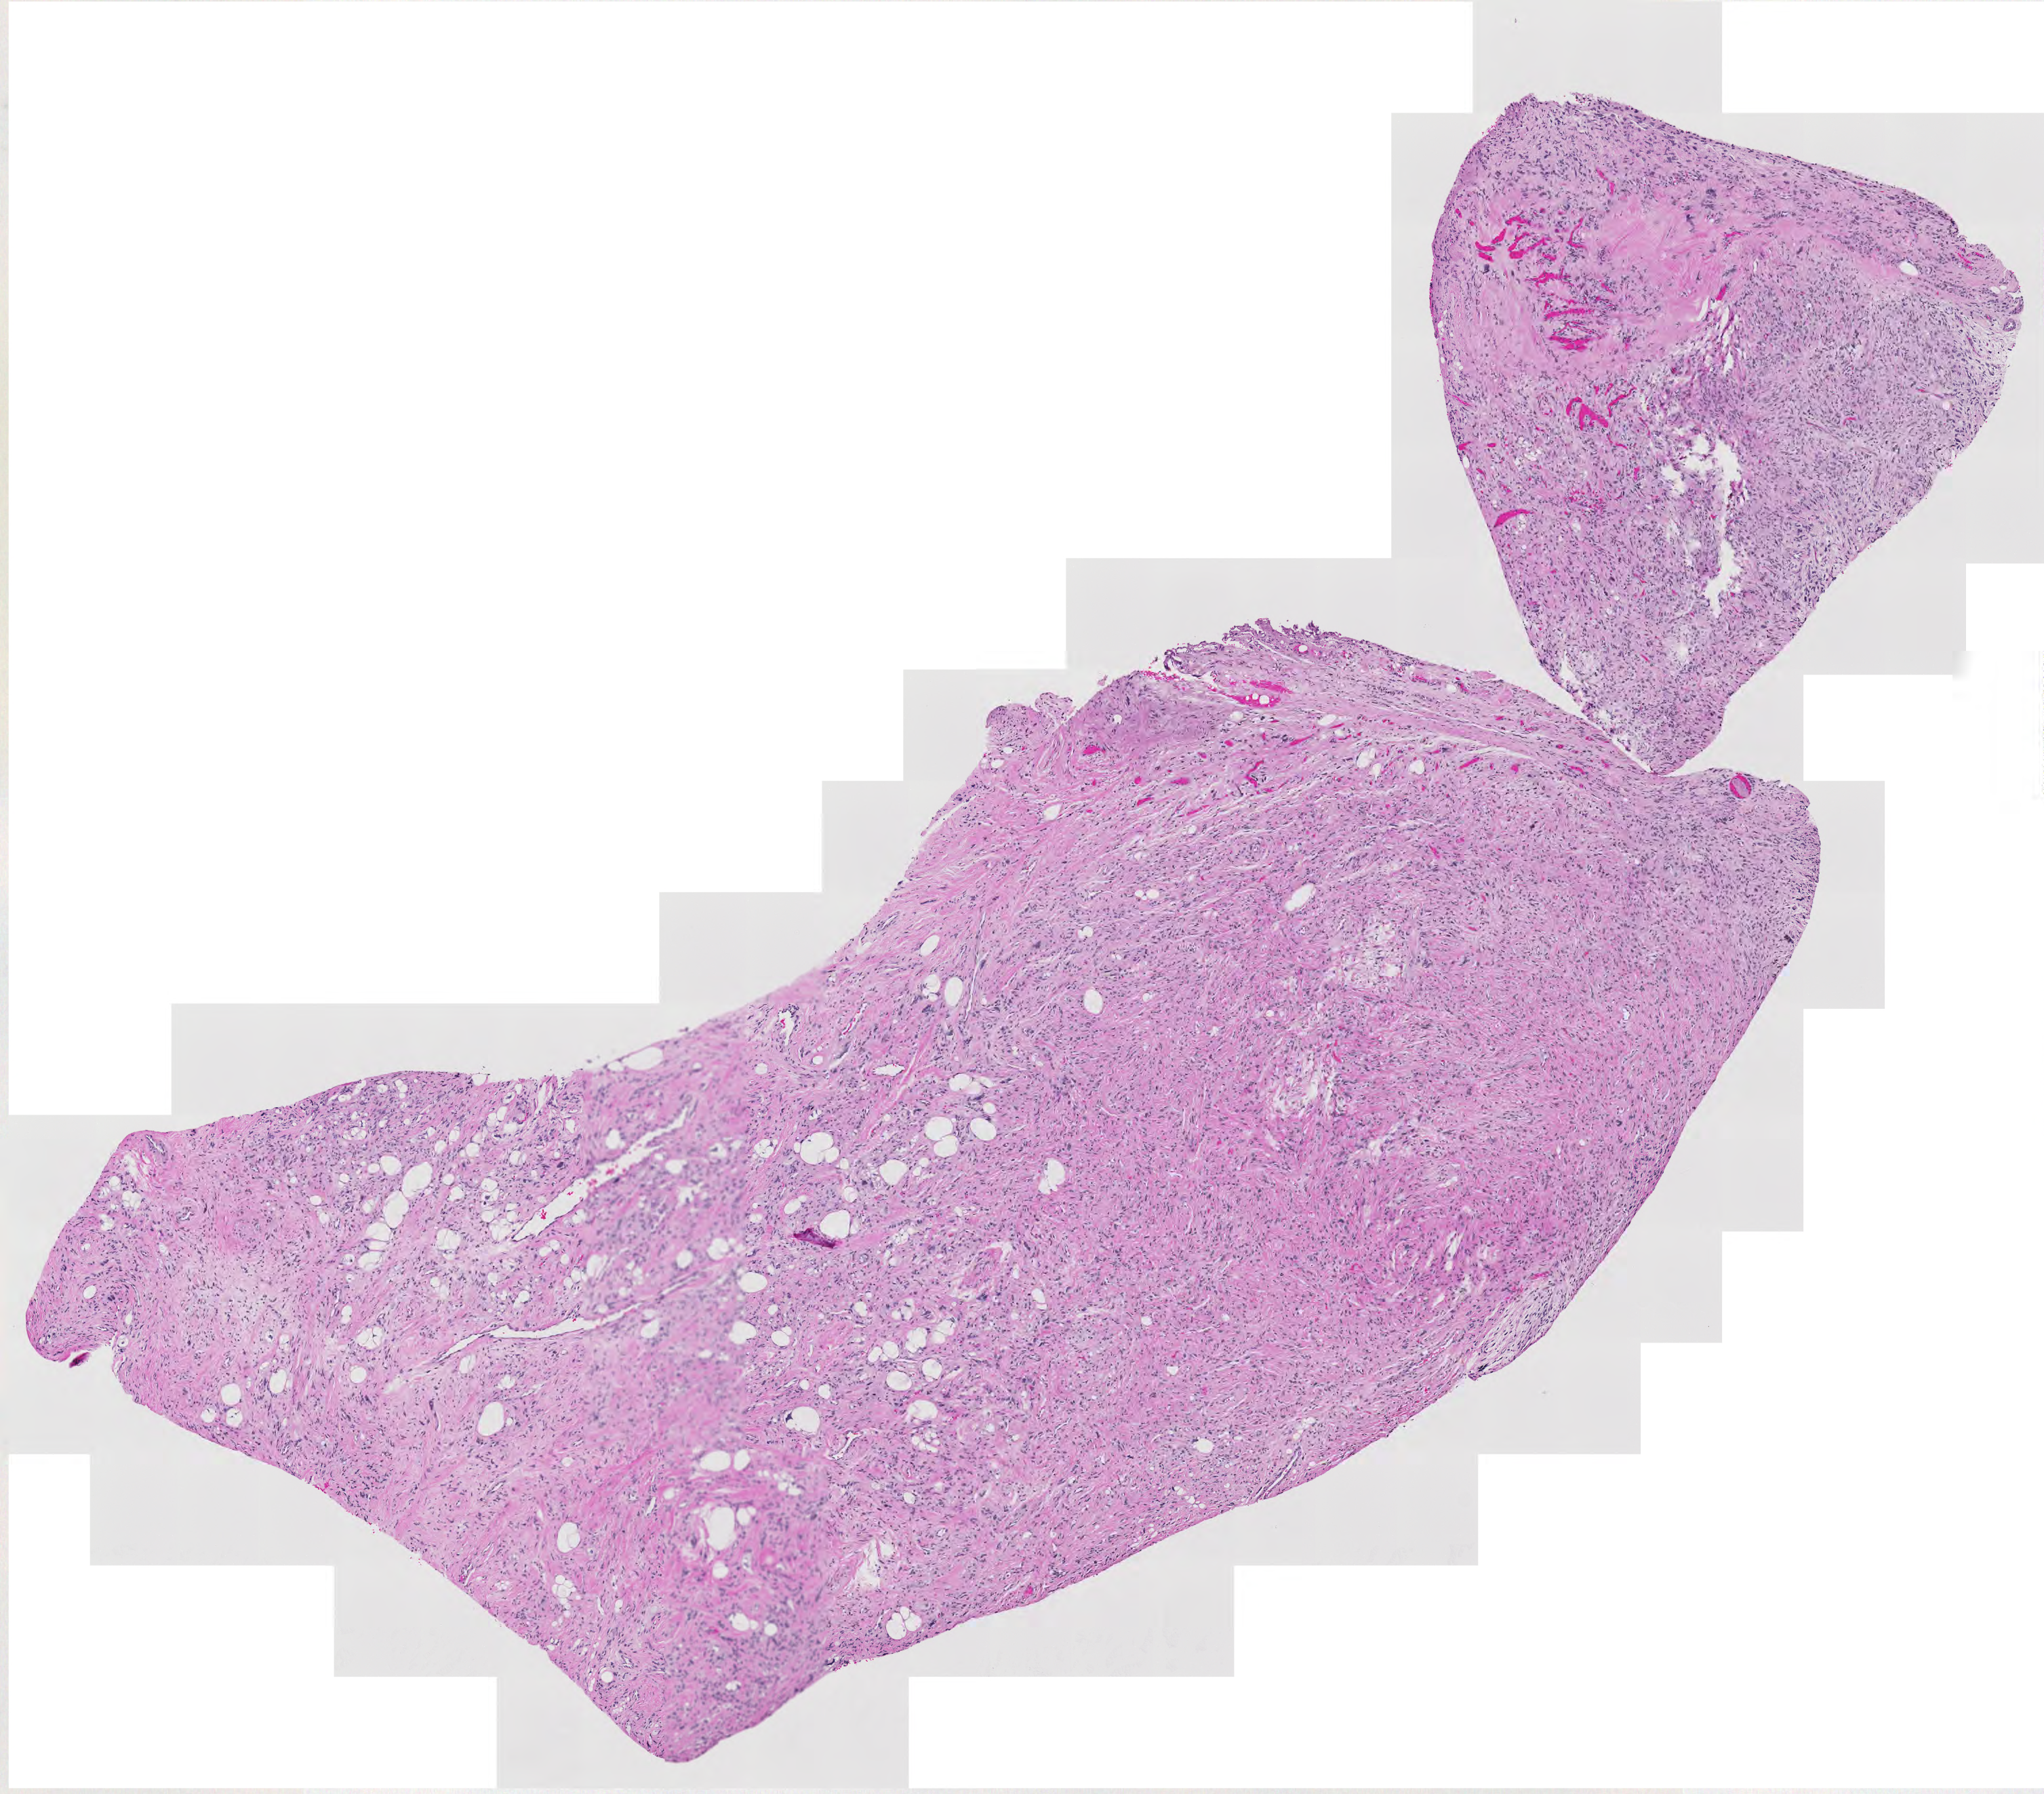
Whole-slide histology image, H&E — low-resolution overview of the scanned area, about 7.8 x 6.8 mm. Tumour tissue sample. Patient: male, age 74 years.
Patient diagnosis (cohort enrolment): sarcoma (site not recorded at cohort level).